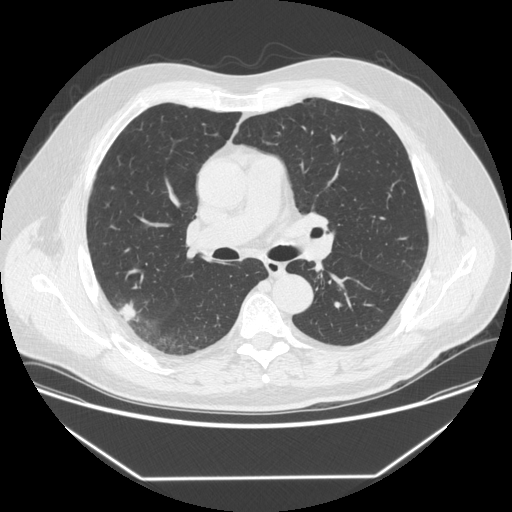
Low-dose screening chest CT, one axial slice; slice 214 of 342 in the series (ordered by position); reconstruction kernel STANDARD; 120 kVp; lung window (W 1500 / L -600 HU); 512 × 512 image matrix.
Structures marked on this image (expert manual segmentation):
- lesion 1 (tumor, upper lobe of right lung): bounding box [x1, y1, x2, y2] px = [119, 304, 136, 323]